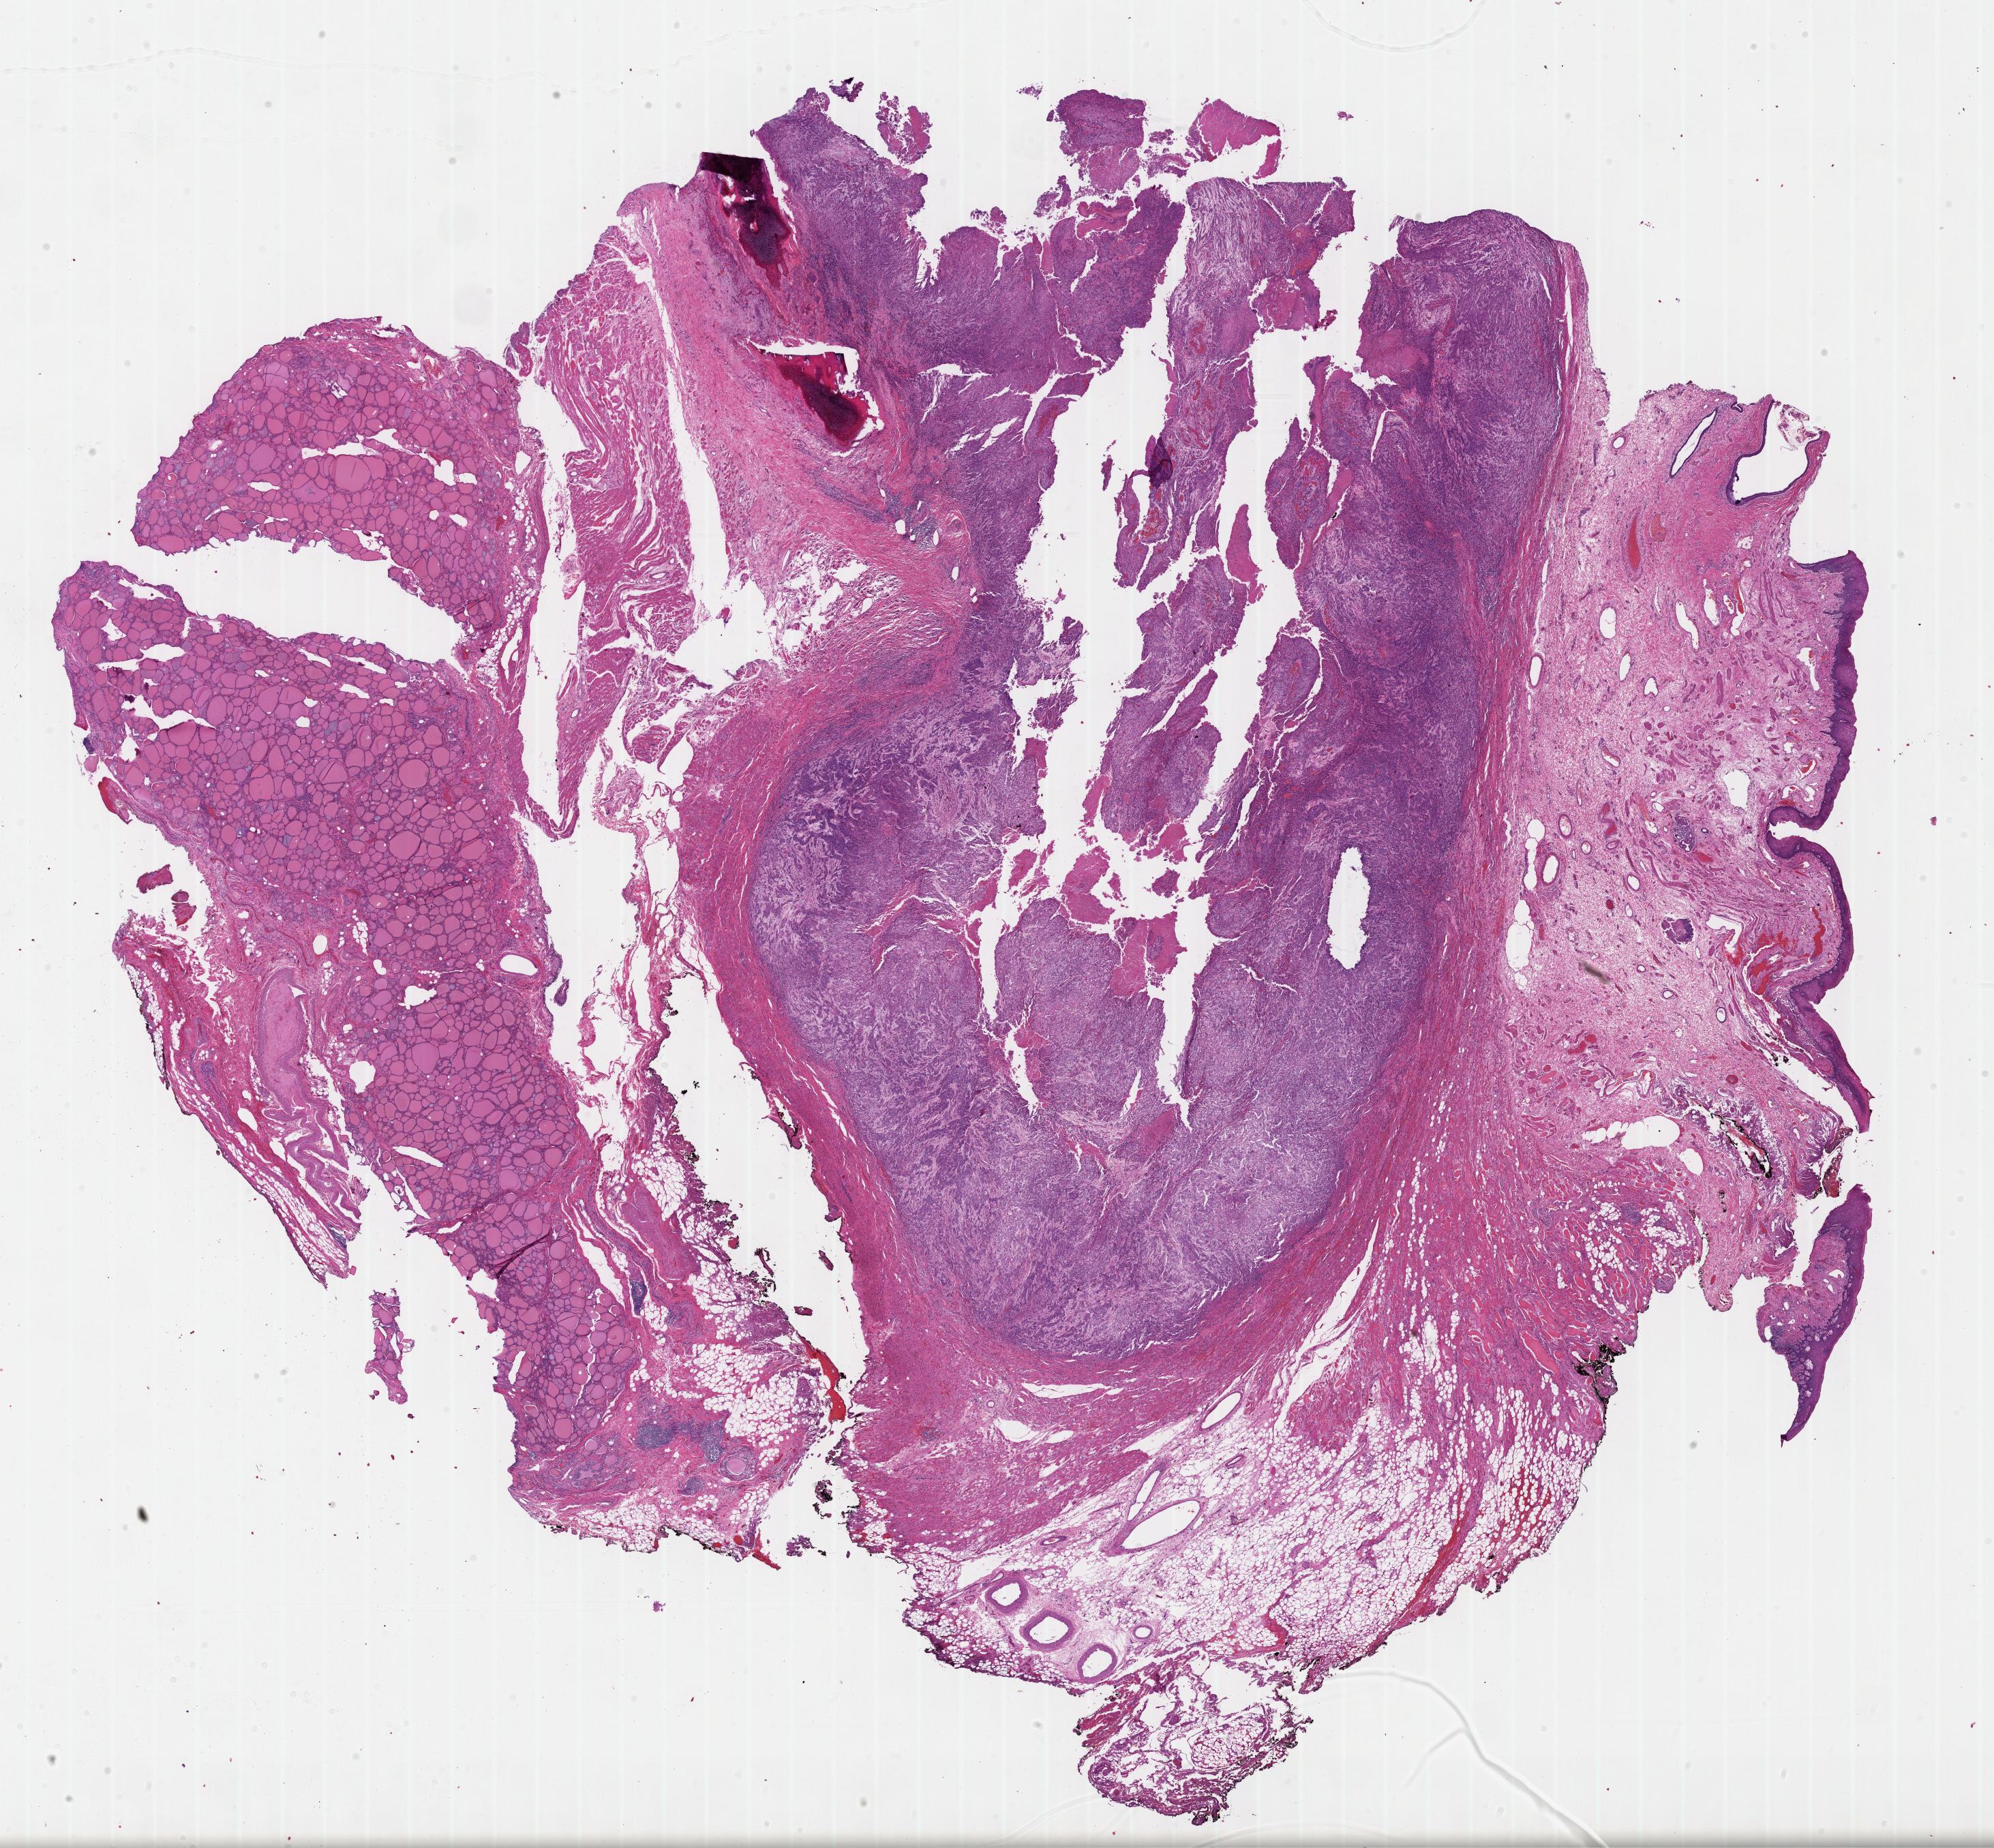
H&E whole-slide image, shown as a low-resolution overview of the whole scanned area (about 23.6 x 21.9 mm, acquisition: 40x scan); formalin-fixed paraffin-embedded (FFPE) diagnostic section; head and neck, primary tumour sample. Patient: male, age at initial diagnosis 64 years. Histologic grade: G3 (poorly differentiated).
- AJCC pathologic stage: IVA (7th edition)
- diagnosis: Squamous cell carcinoma, NOS (hypopharynx, NOS)